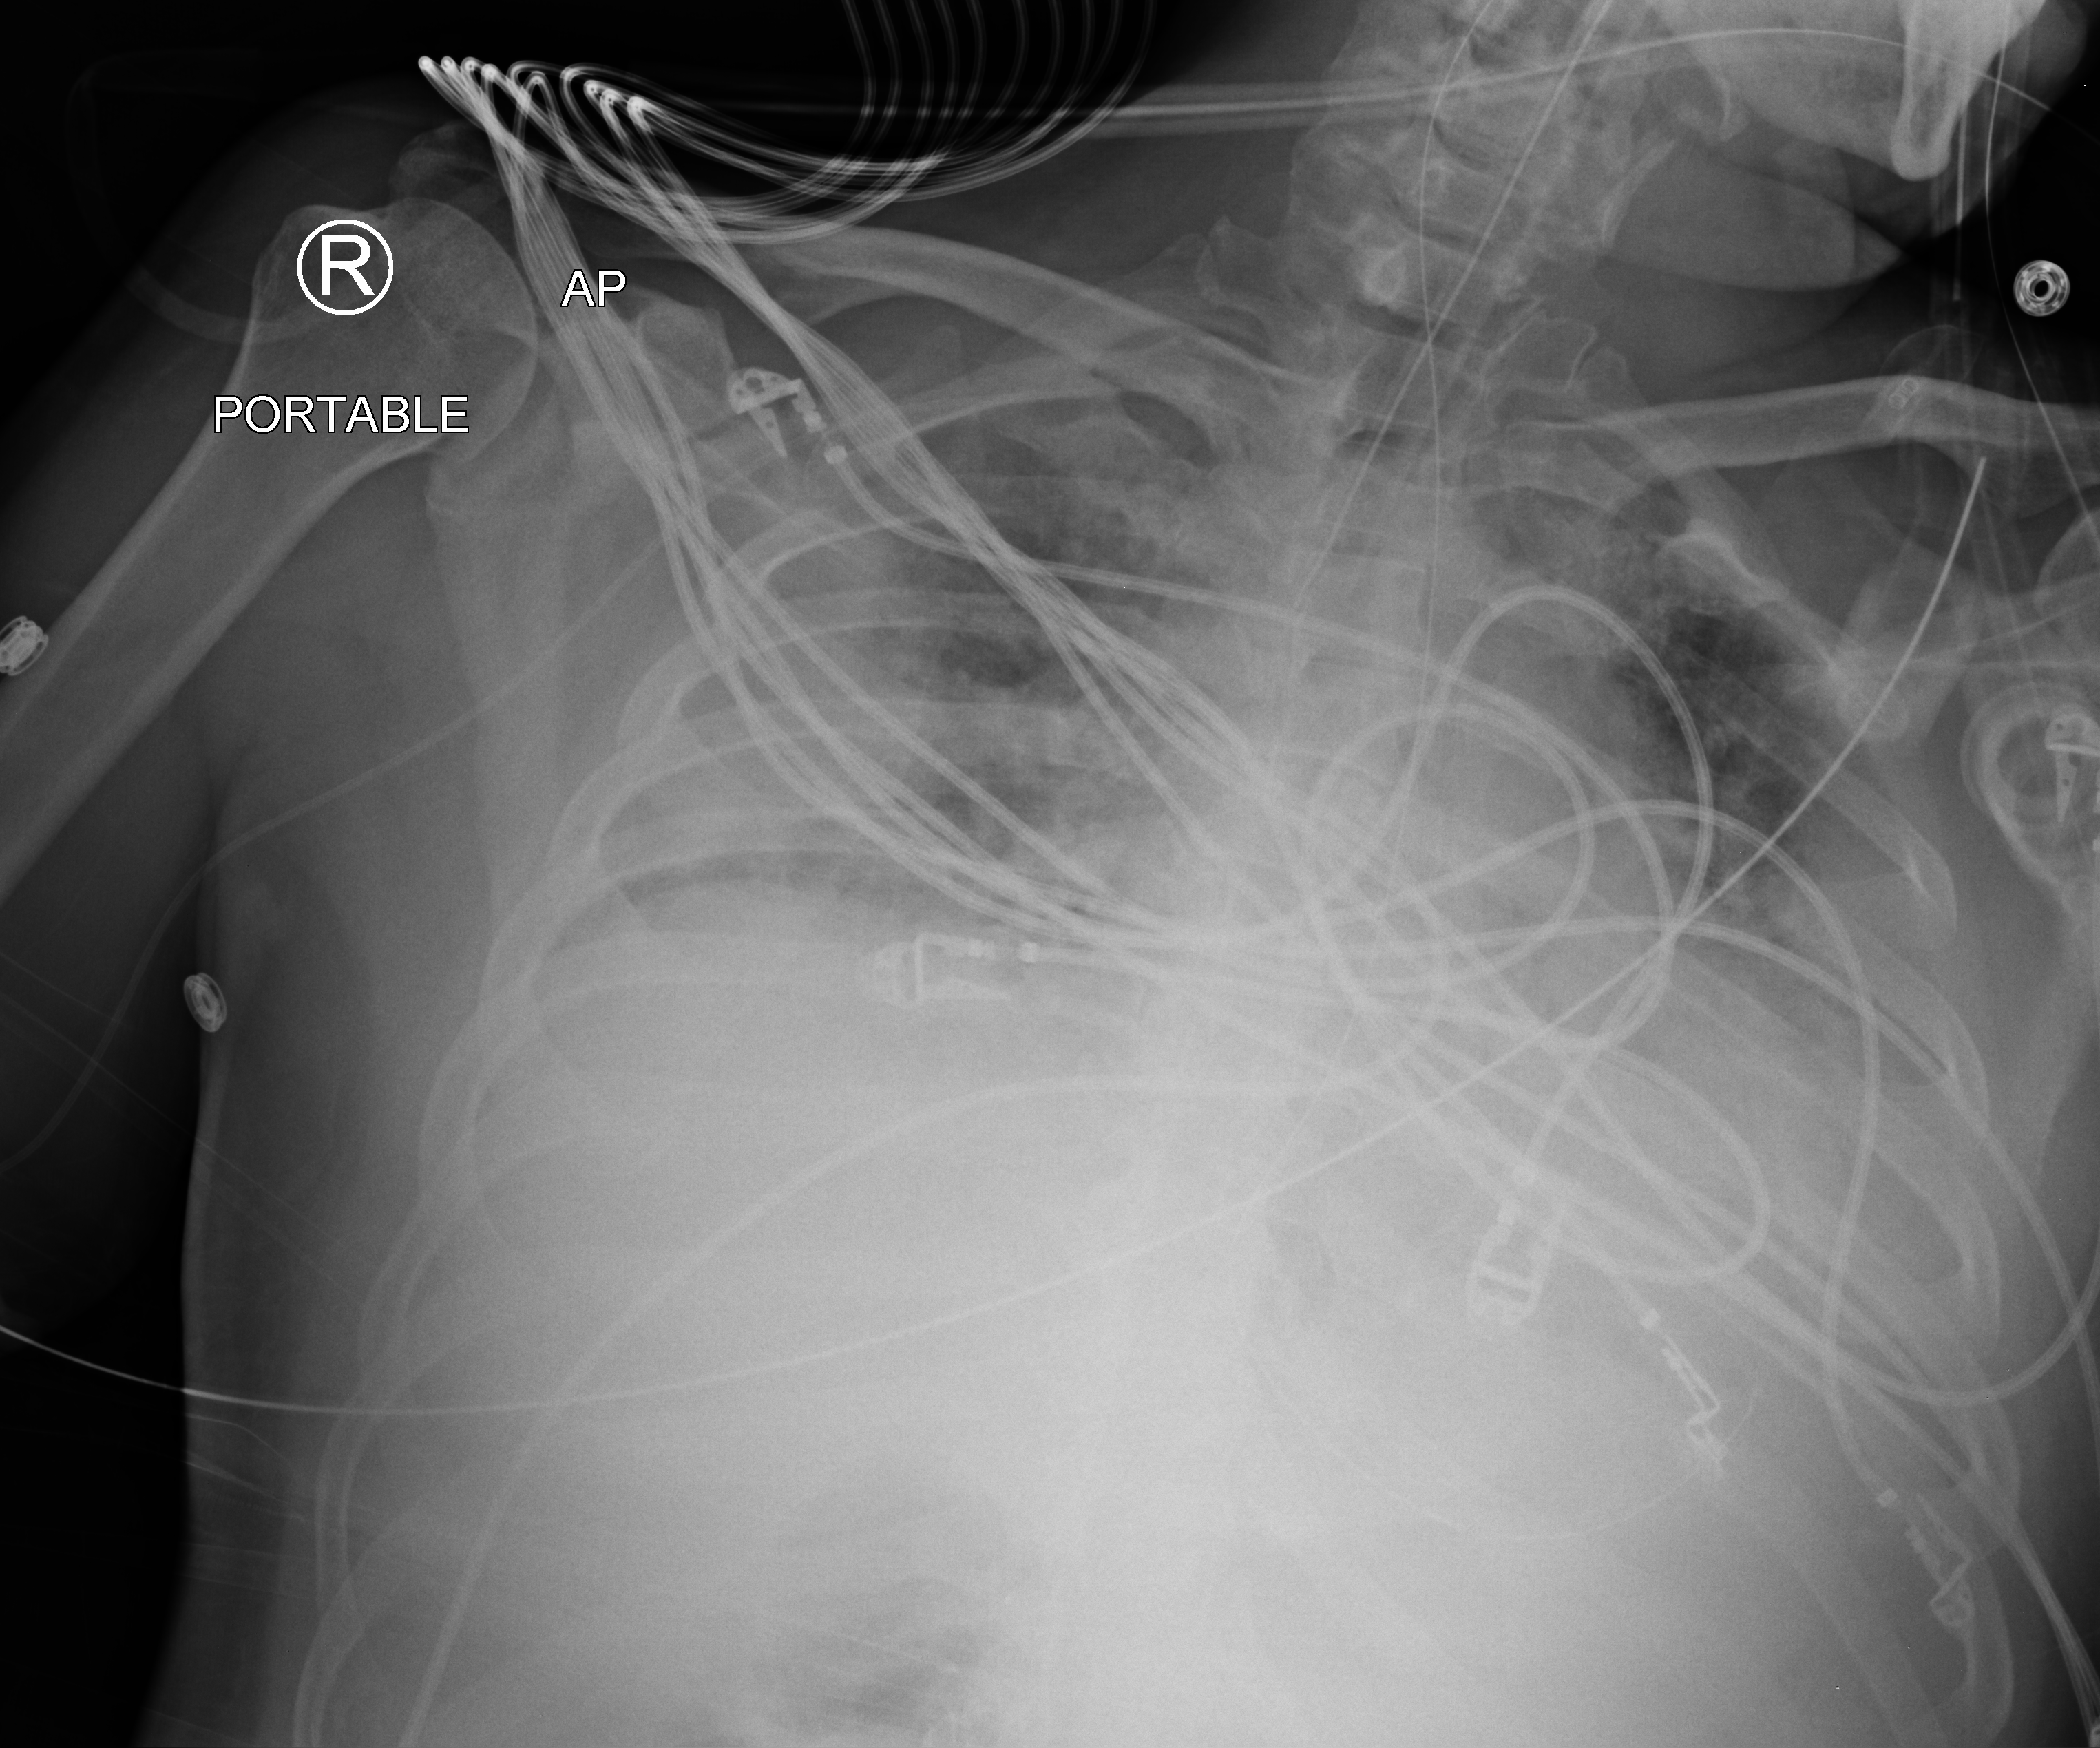
Bedside chest radiograph (computed radiography), anteroposterior (AP) projection. Male patient hospitalised with COVID-19, age 60–74 years.
Admission-level facts for this patient (not findings on this image; timing relative to this image not recorded): smoking status (admission record): never; length of hospital stay: 26 days; mechanically ventilated during this hospital stay: yes.